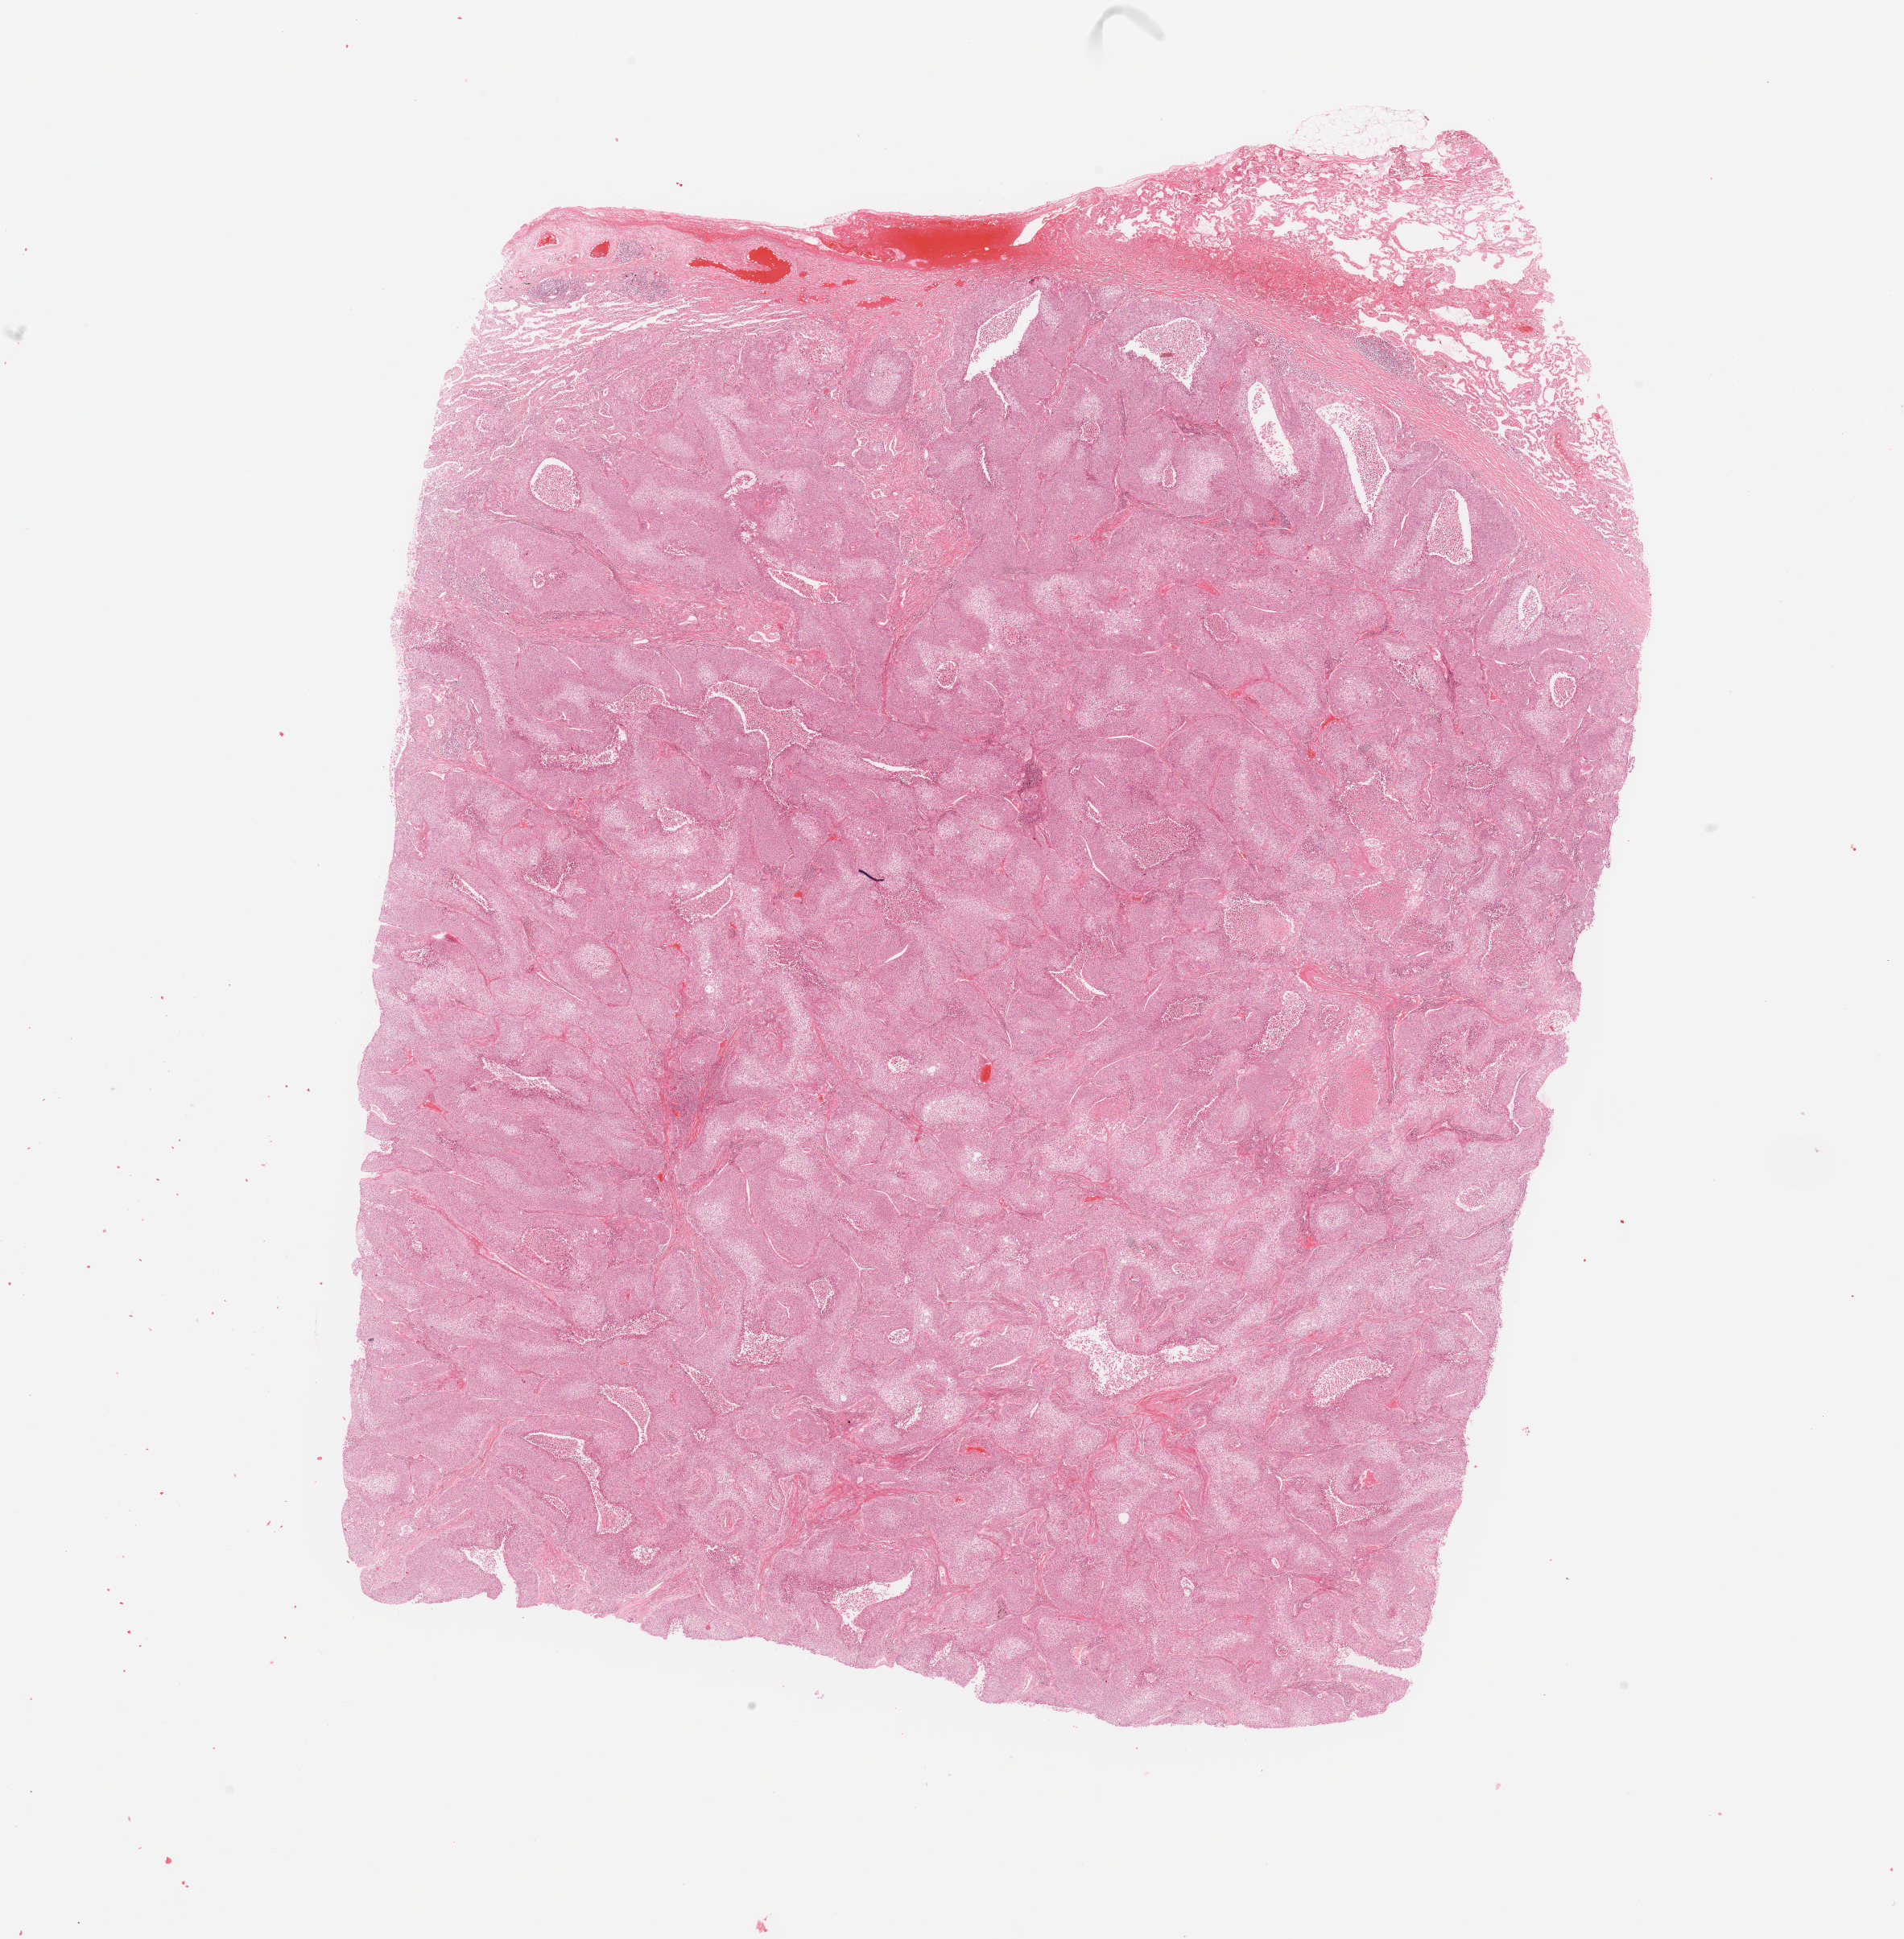
Whole-slide histology image, H&E-stained, low-resolution overview of the scanned area, about 18.7 x 19.1 mm (acquisition: 20x scan), tumour tissue sample, lung. Patient: male, age 59 years. Histologic grade: G2 (moderately differentiated).
Diagnosis: Squamous cell carcinoma, NOS. AJCC pathologic stage: IIB.